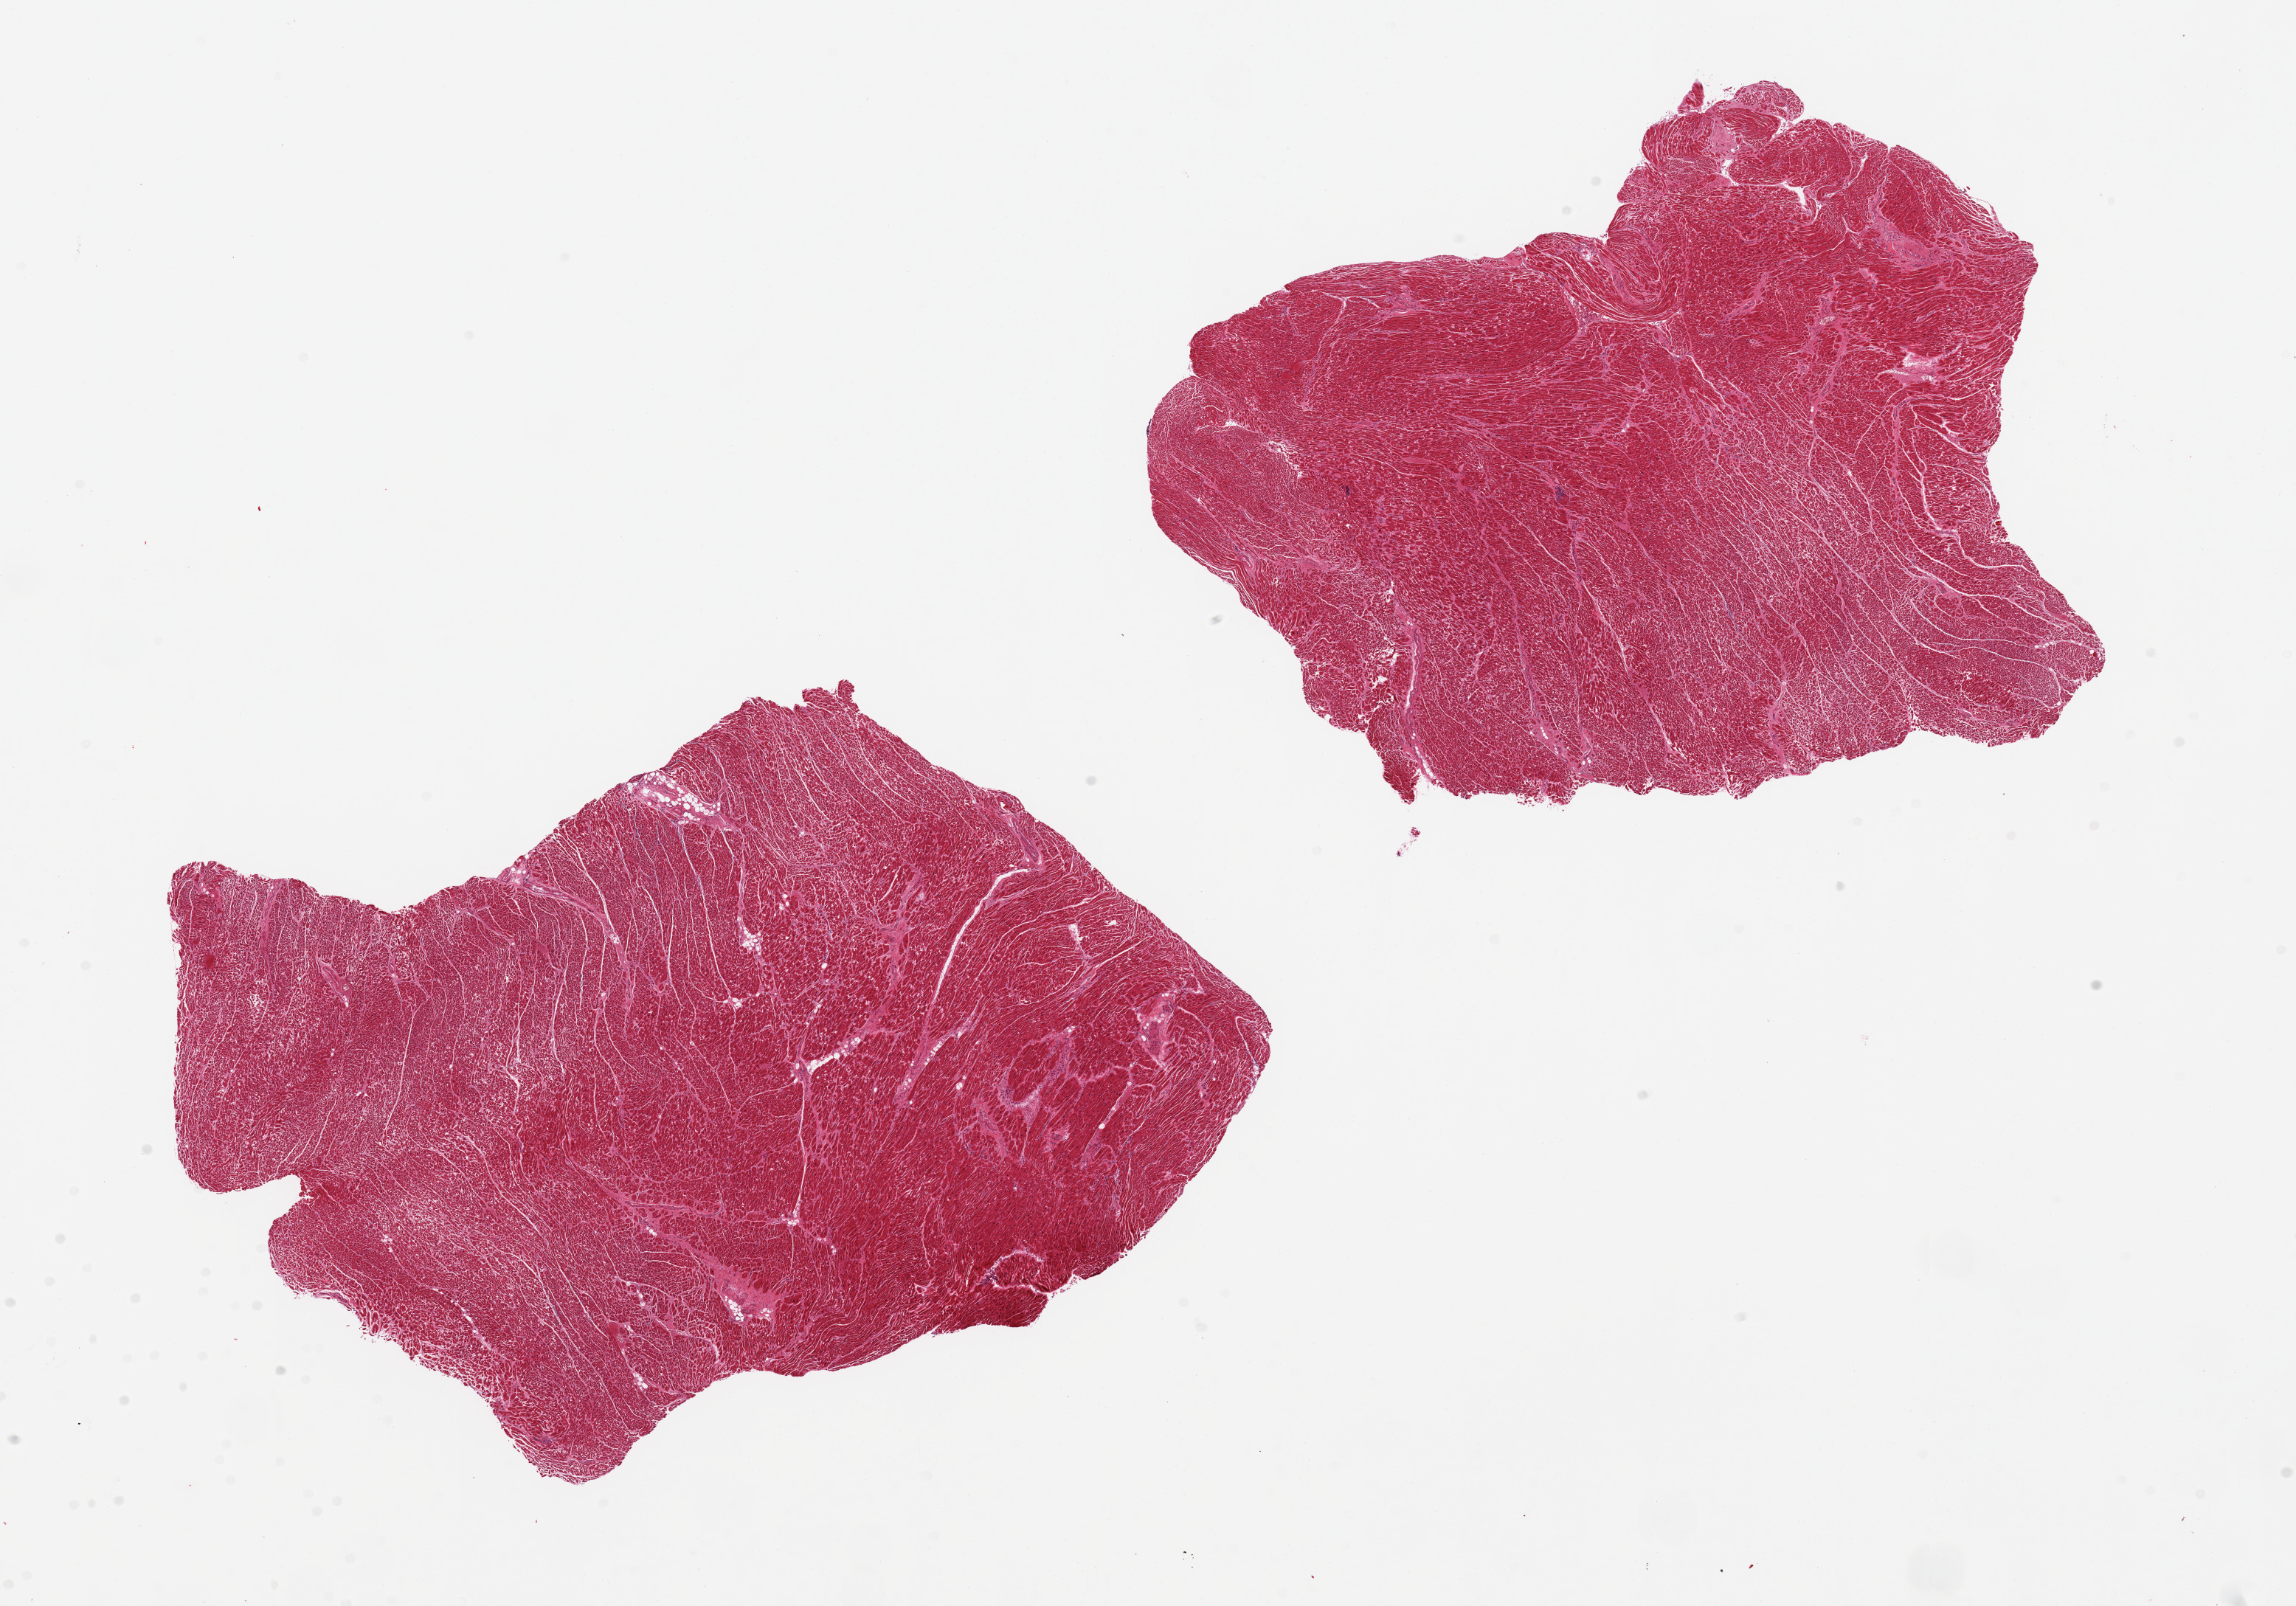
Digitized haematoxylin and eosin-stained section, a low-resolution overview of the entire scanned area, about 24.6 x 17.2 mm; PAXgene-fixed, paraffin-embedded tissue; sampled site (target tissue): heart; tissue donor sample.
Pathologist's review note for this sample: 2 pieces; hypertrophied fibers; hypereosinophilic areas suggest ischemia.